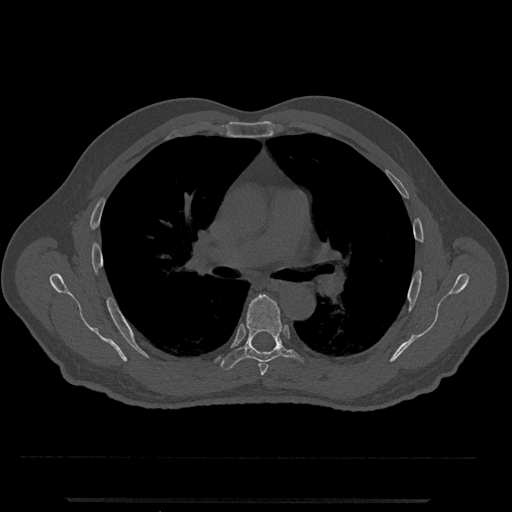
CT including the spine, one axial slice. Slice 747 of 797 in the series (ordered by position). Bone window (W 1800 / L 400 HU). 512 × 512 image matrix, field of view 419 × 419 mm. Male patient, age 63 years. From the clinical record (not read from this slice): primary cancer: prostate.
Structures marked on this image (semi-automatic segmentation, software-assisted and operator-edited):
- T5 vertebra: box from (x=259, y=362) to (x=268, y=375) px
- T6 vertebra: (x=220, y=295)–(x=305, y=370)